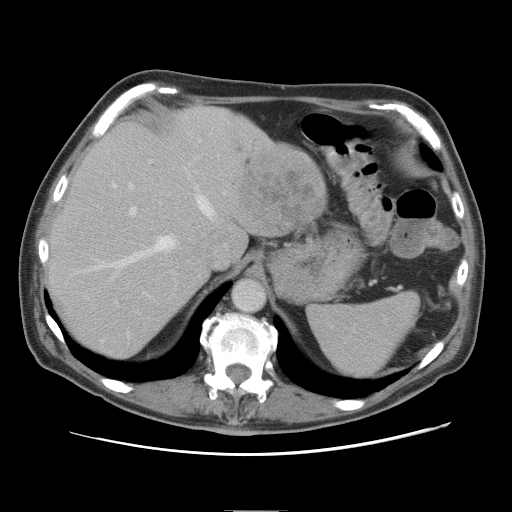
Contrast-enhanced abdominal CT, one axial slice. Position 60 of 89 along the scan axis. 120 kVp. Intravenous contrast given. Soft-tissue window (W 400 / L 40 HU). 5 mm slice thickness. 512 × 512 image matrix, field of view 375 × 375 mm. Male patient, age 69 years. Case-level facts recorded for this patient, not image findings: diagnosis: colorectal cancer liver metastases, imaged before liver resection; multiple liver metastases: no; largest metastasis: 8.5 cm; disease in both lobes: no.
Annotated regions visible in this slice (expert manual segmentation):
- hepatic veins: bounding box <92,169,216,269> (left, top, right, bottom; pixels)
- liver: <50,106,326,355>
- planned liver remnant (the part of the liver to remain after resection): <50,106,246,355>
- portal vein (with intrahepatic branches): <129,141,207,216>
- liver metastasis: <240,164,318,230>